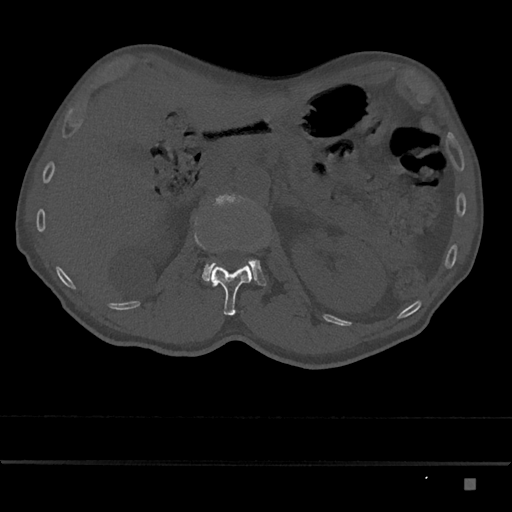
CT including the spine, one axial slice; position 522 of 797 along the scan axis; bone window (W 1800 / L 400 HU); 0.5 mm slice thickness; 512 × 512 image matrix, field of view 390 × 390 mm. Male patient, age 72 years. From the clinical record (not read from this slice): primary cancer: prostate.
Structures marked on this image (semi-automatically segmented with operator editing):
- L1 vertebra: bounding box (x1, y1, x2, y2) in pixels: (208, 246, 252, 316)
- L2 vertebra: (202, 194, 266, 286)